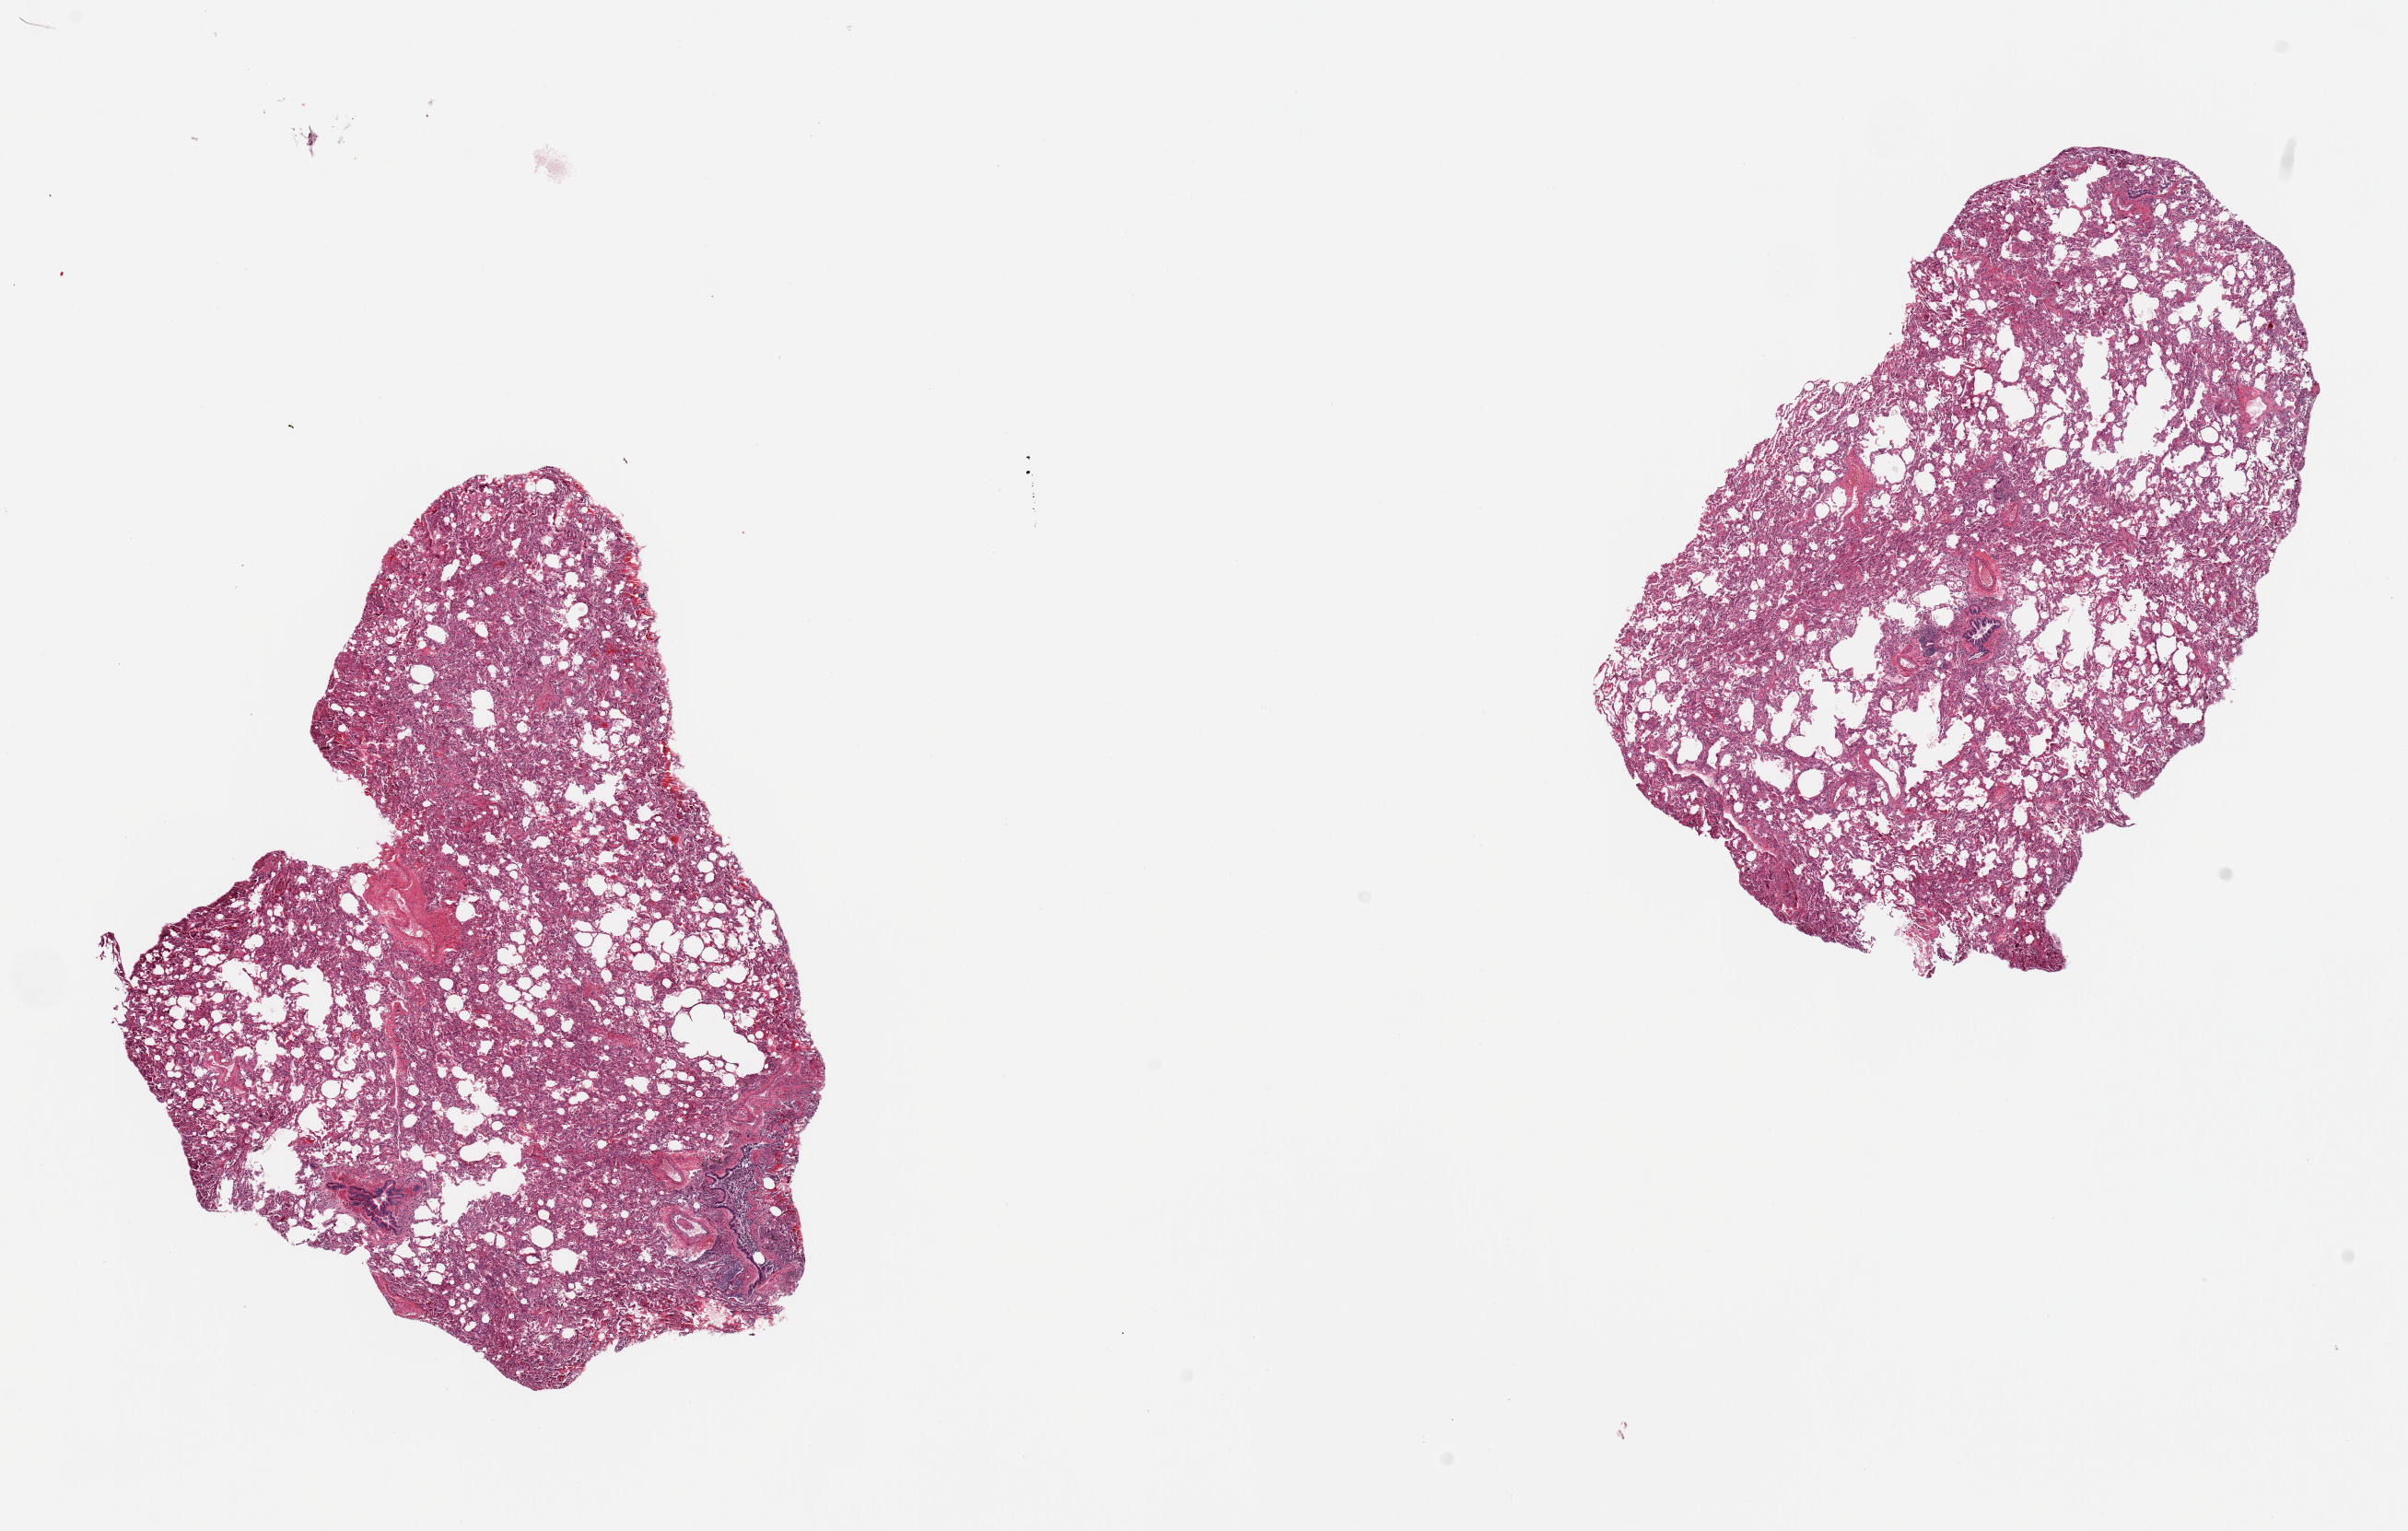
Haematoxylin and eosin whole-slide image, brightfield, a low-resolution overview of the entire scanned area, about 20.7 x 13.1 mm, PAXgene-fixed paraffin-embedded (PFPE) section, section of lung (target tissue), donor tissue sample. Male donor.
Review note (as recorded): 2 pieces.